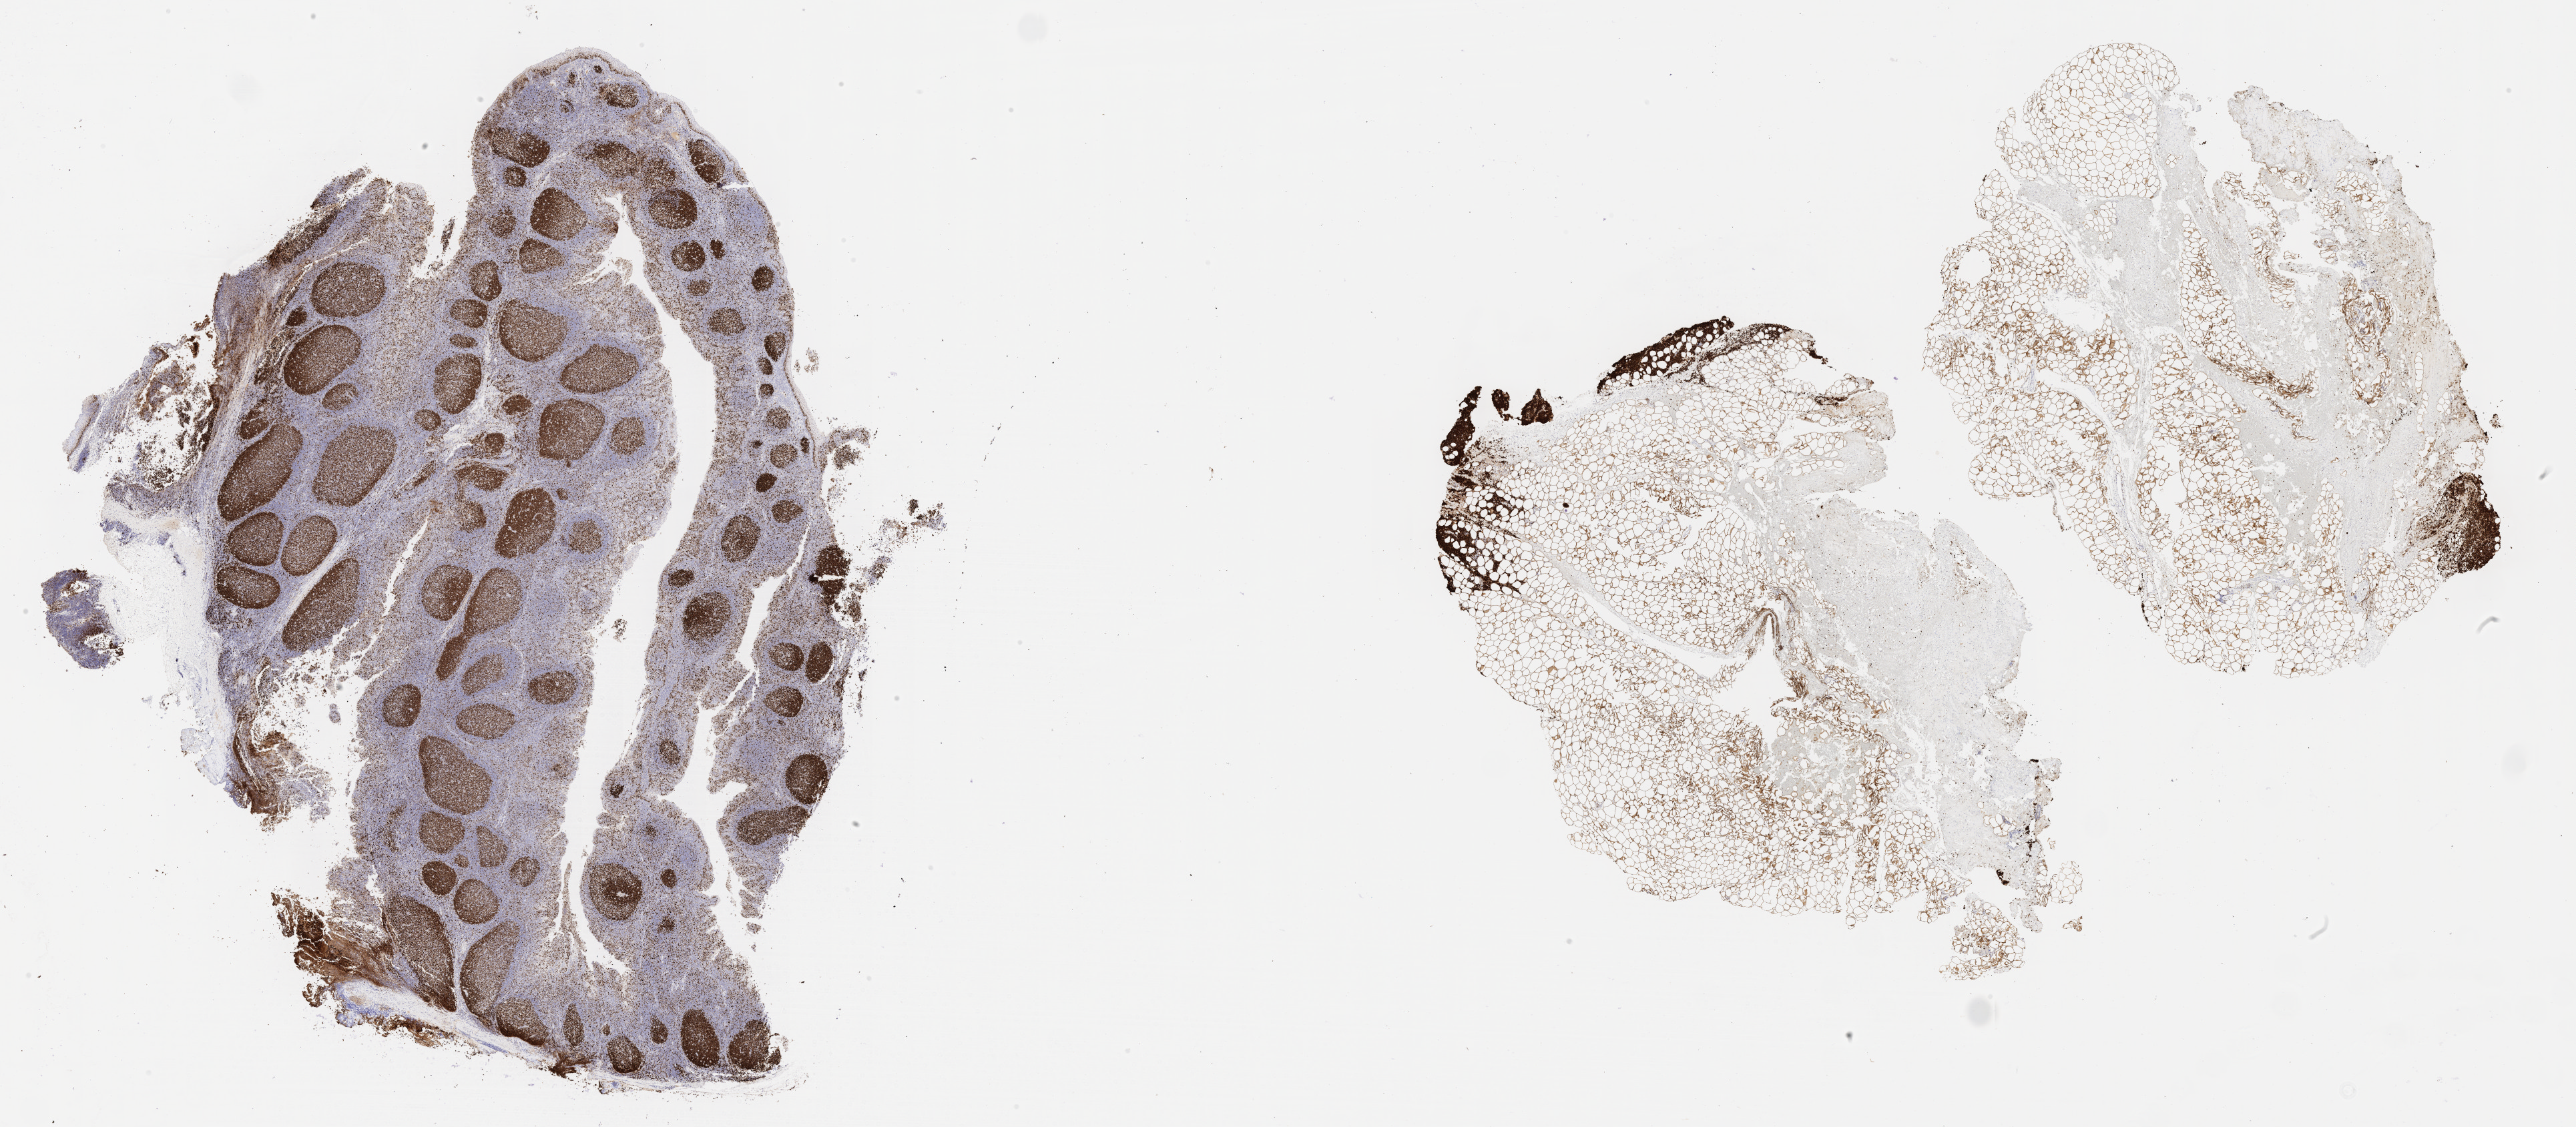
Whole-slide image, immunohistochemical stain for Ki-67 — whole scanned area (about 31.2 x 13.7 mm) shown as a low-resolution overview. Specimen: tumor tissue. Site: upper limb lymph node. Patient male; aged 76.
* diagnosis: Burkitt lymphoma, NOS